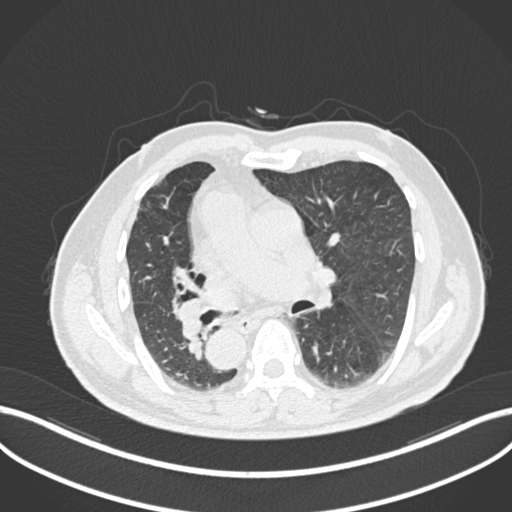
Chest CT, one axial slice; slice 120 of 206 in the series (ordered by position); reconstruction kernel B30f; lung window (W 1500 / L -600 HU); 1 mm slice thickness; 512 × 512 image matrix, field of view 400 × 400 mm. Male patient, age 67 years. Case-level facts recorded for this patient, not image findings: clinical TNM (as recorded): T2a N0 M0.
Annotated regions visible in this slice (bounding box drawn by a radiologist):
- lung tumour (recorded histology: squamous cell carcinoma): bounding box [x1, y1, x2, y2] px = [171, 294, 208, 340]